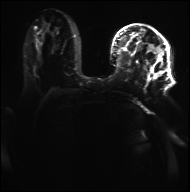
Breast MRI, one axial slice; slice 13 of 36 in the series (ordered by position); diffusion-weighted series; image 2 of 4 stored at this slice position (different b-values; order by instance number); 3 T; 4 mm slice thickness; 190 × 192 image matrix. Female patient.
Structures marked on this image (outlined manually by an expert reader):
- tumour on diffusion-weighted imaging: bounding box <46,50,61,57> (left, top, right, bottom; pixels)